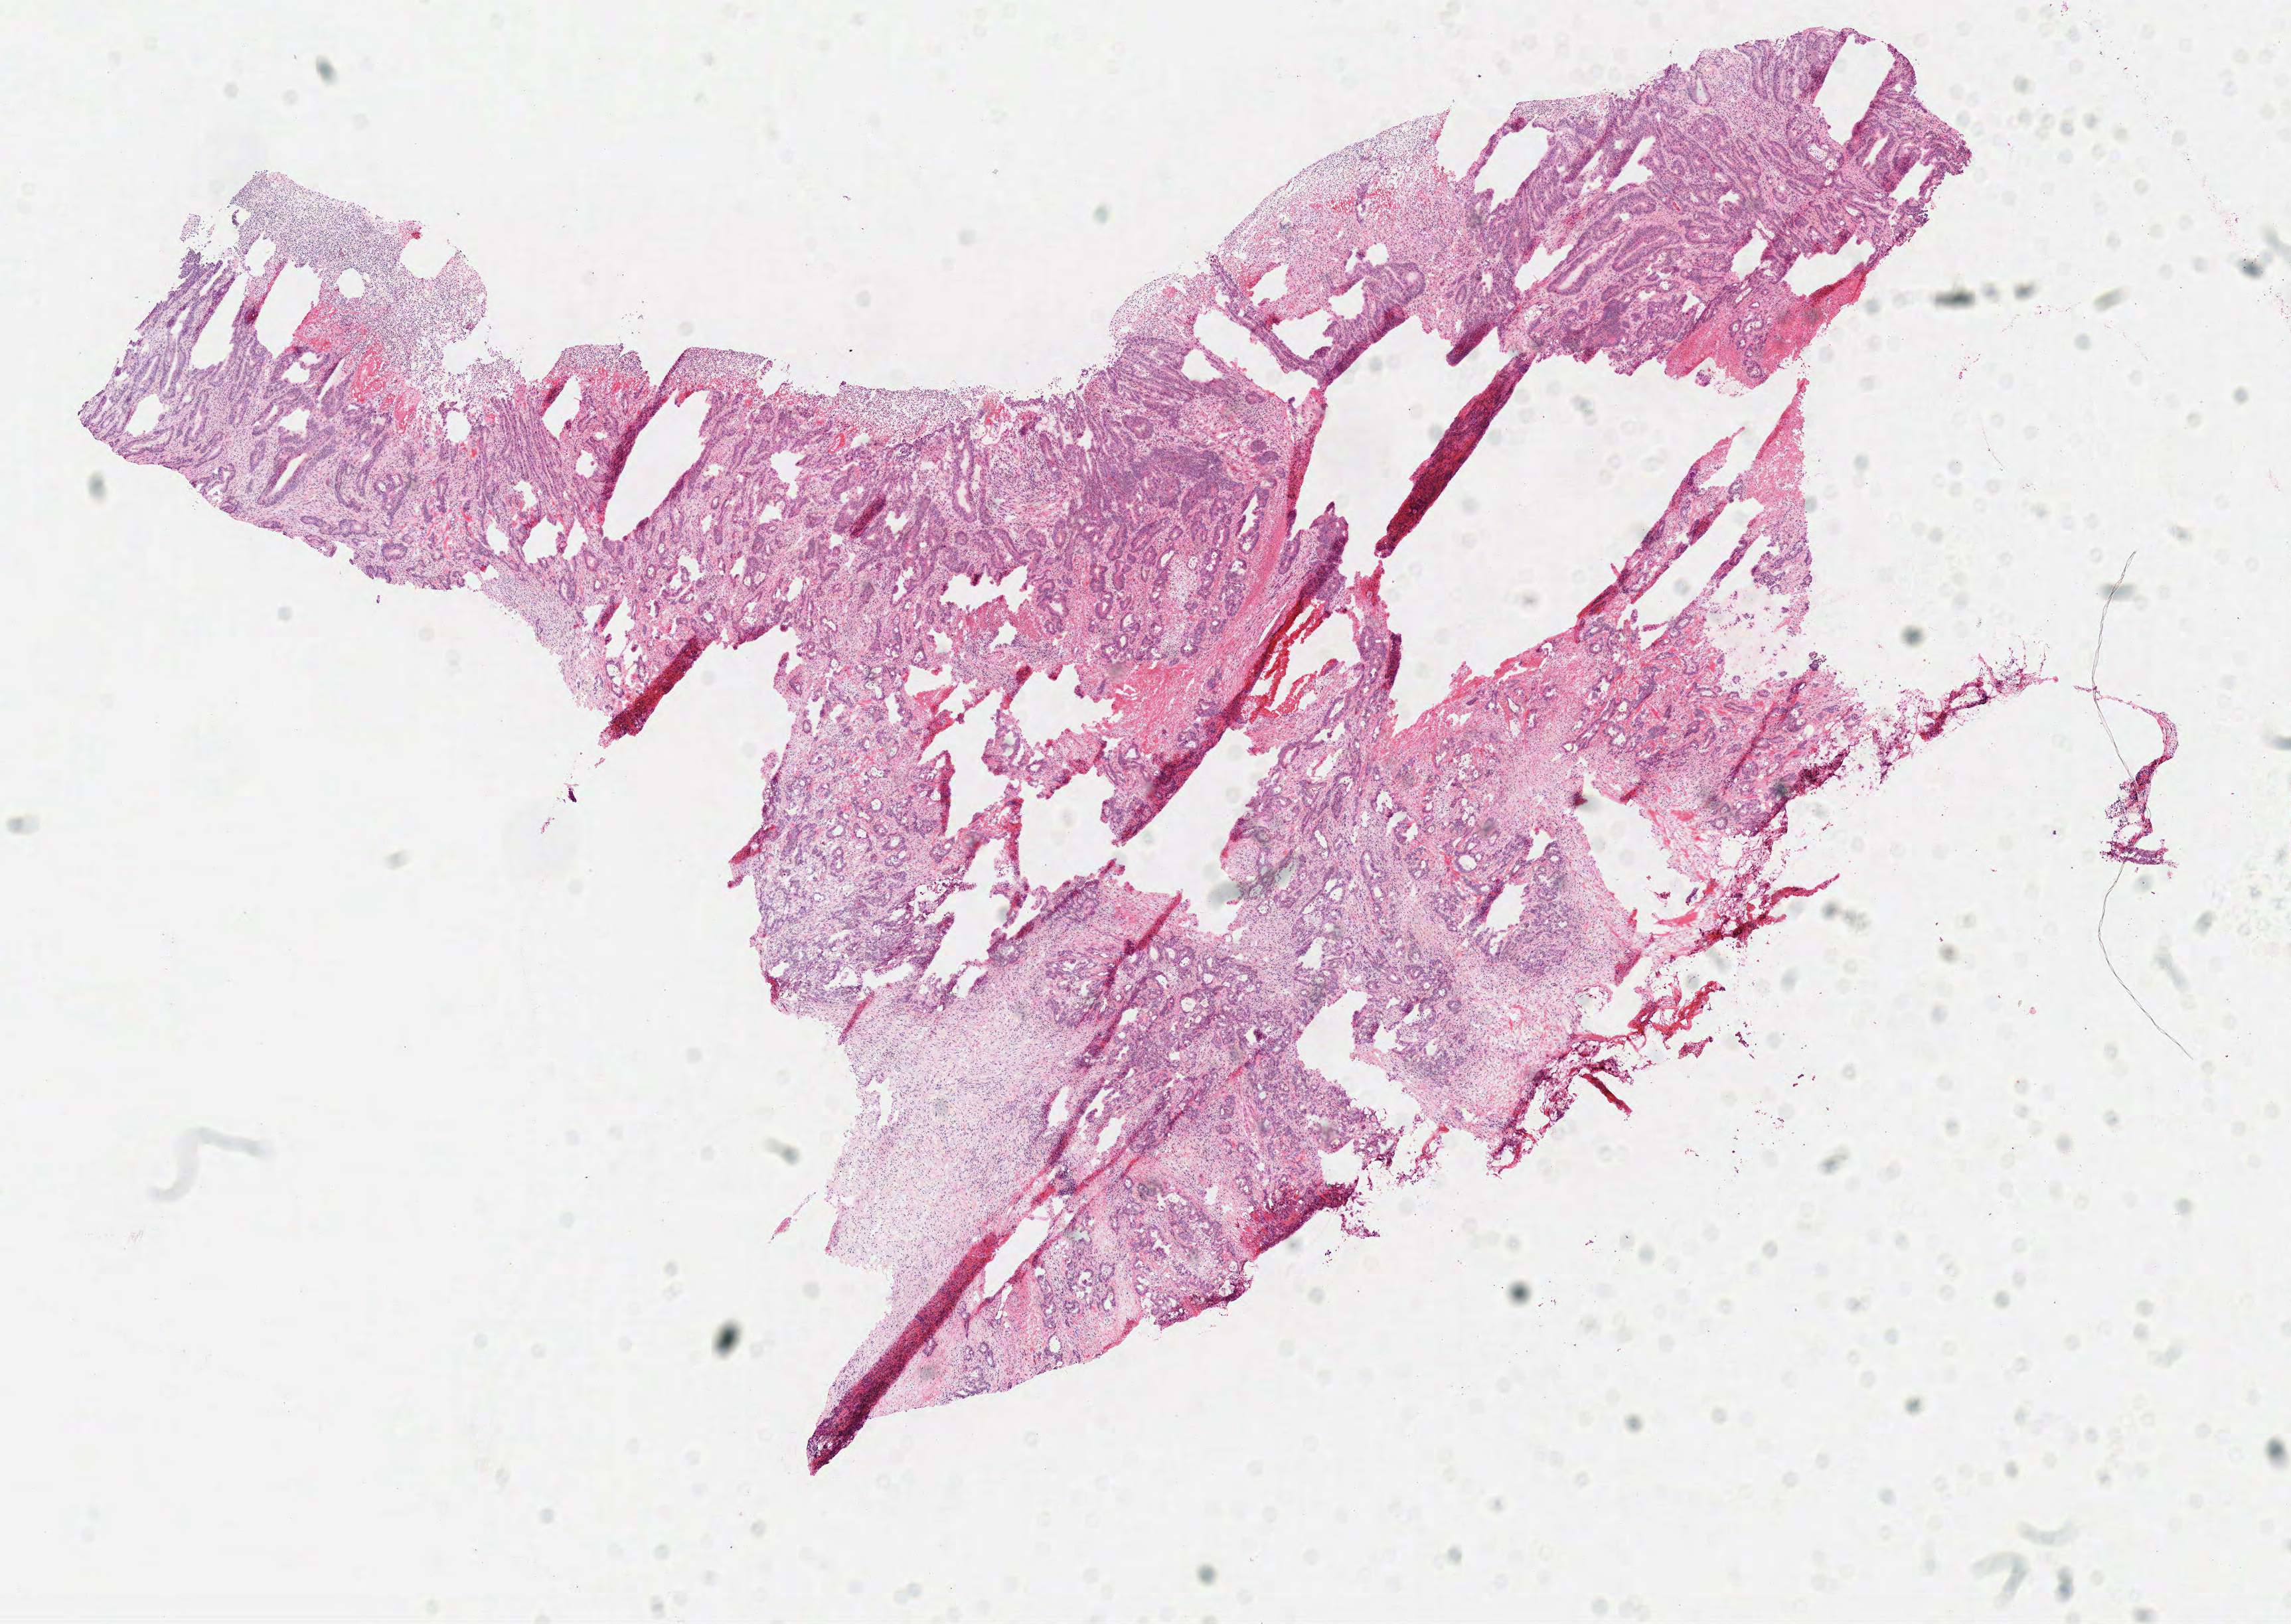
Whole-slide histology image, H&E-stained, whole scanned area (about 13.6 x 9.6 mm, slide scanned at 40x) shown as a low-resolution overview. Frozen section from the top of the tissue portion. Sample: primary tumour, colon. Female, age 59 years at initial diagnosis. Composition of this section per pathologist review: tumour cells 95%, tumour nuclei 75%, normal cells 0%, stromal cells 0%, necrosis 5%. Inflammatory infiltration, as recorded: lymphocyte infiltration 5%, monocyte infiltration 2%, neutrophil infiltration 10%.
AJCC pathologic stage: IVA (7th edition). Diagnosis: Adenocarcinoma, NOS.